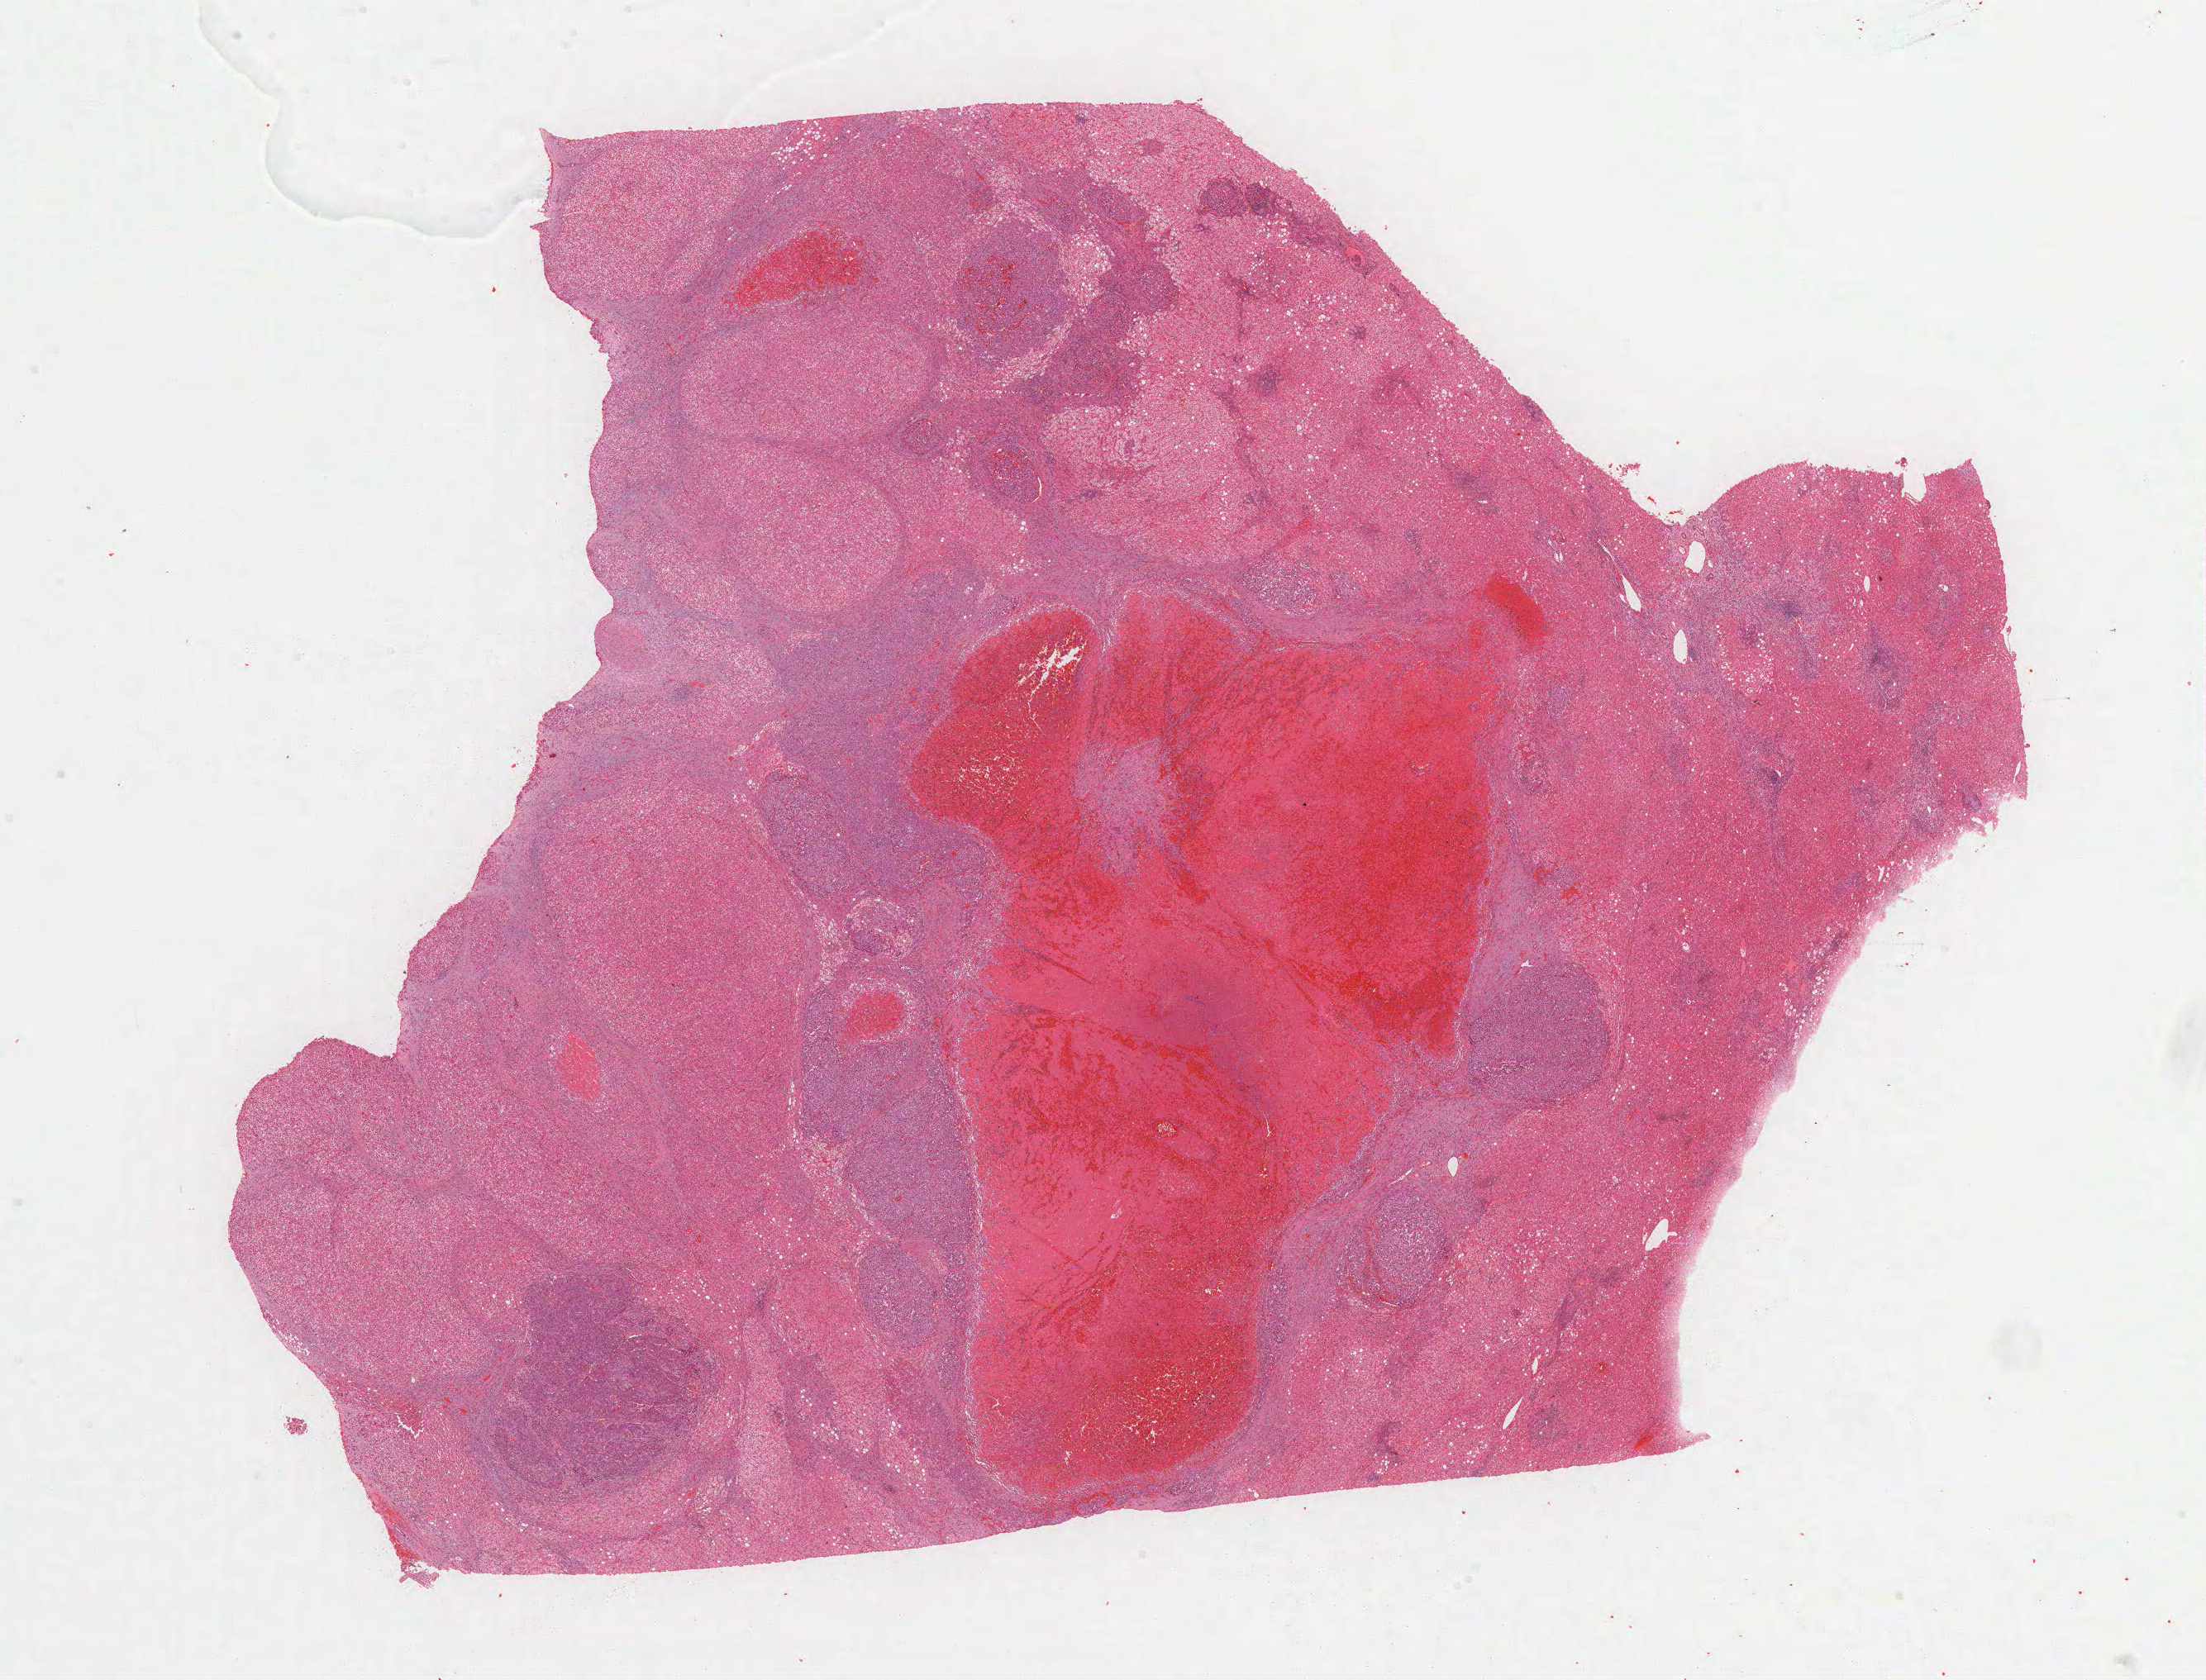
Whole-slide histology image, Hematoxylin and eosin (H&E) stained, low-resolution overview of the scanned area, about 21.6 x 16.4 mm. FFPE section. Sample: primary tumour, liver. Male patient; age at initial diagnosis 58 years. Histologic grade: G2 (moderately differentiated).
Pathologic diagnosis: Hepatocellular carcinoma, NOS.